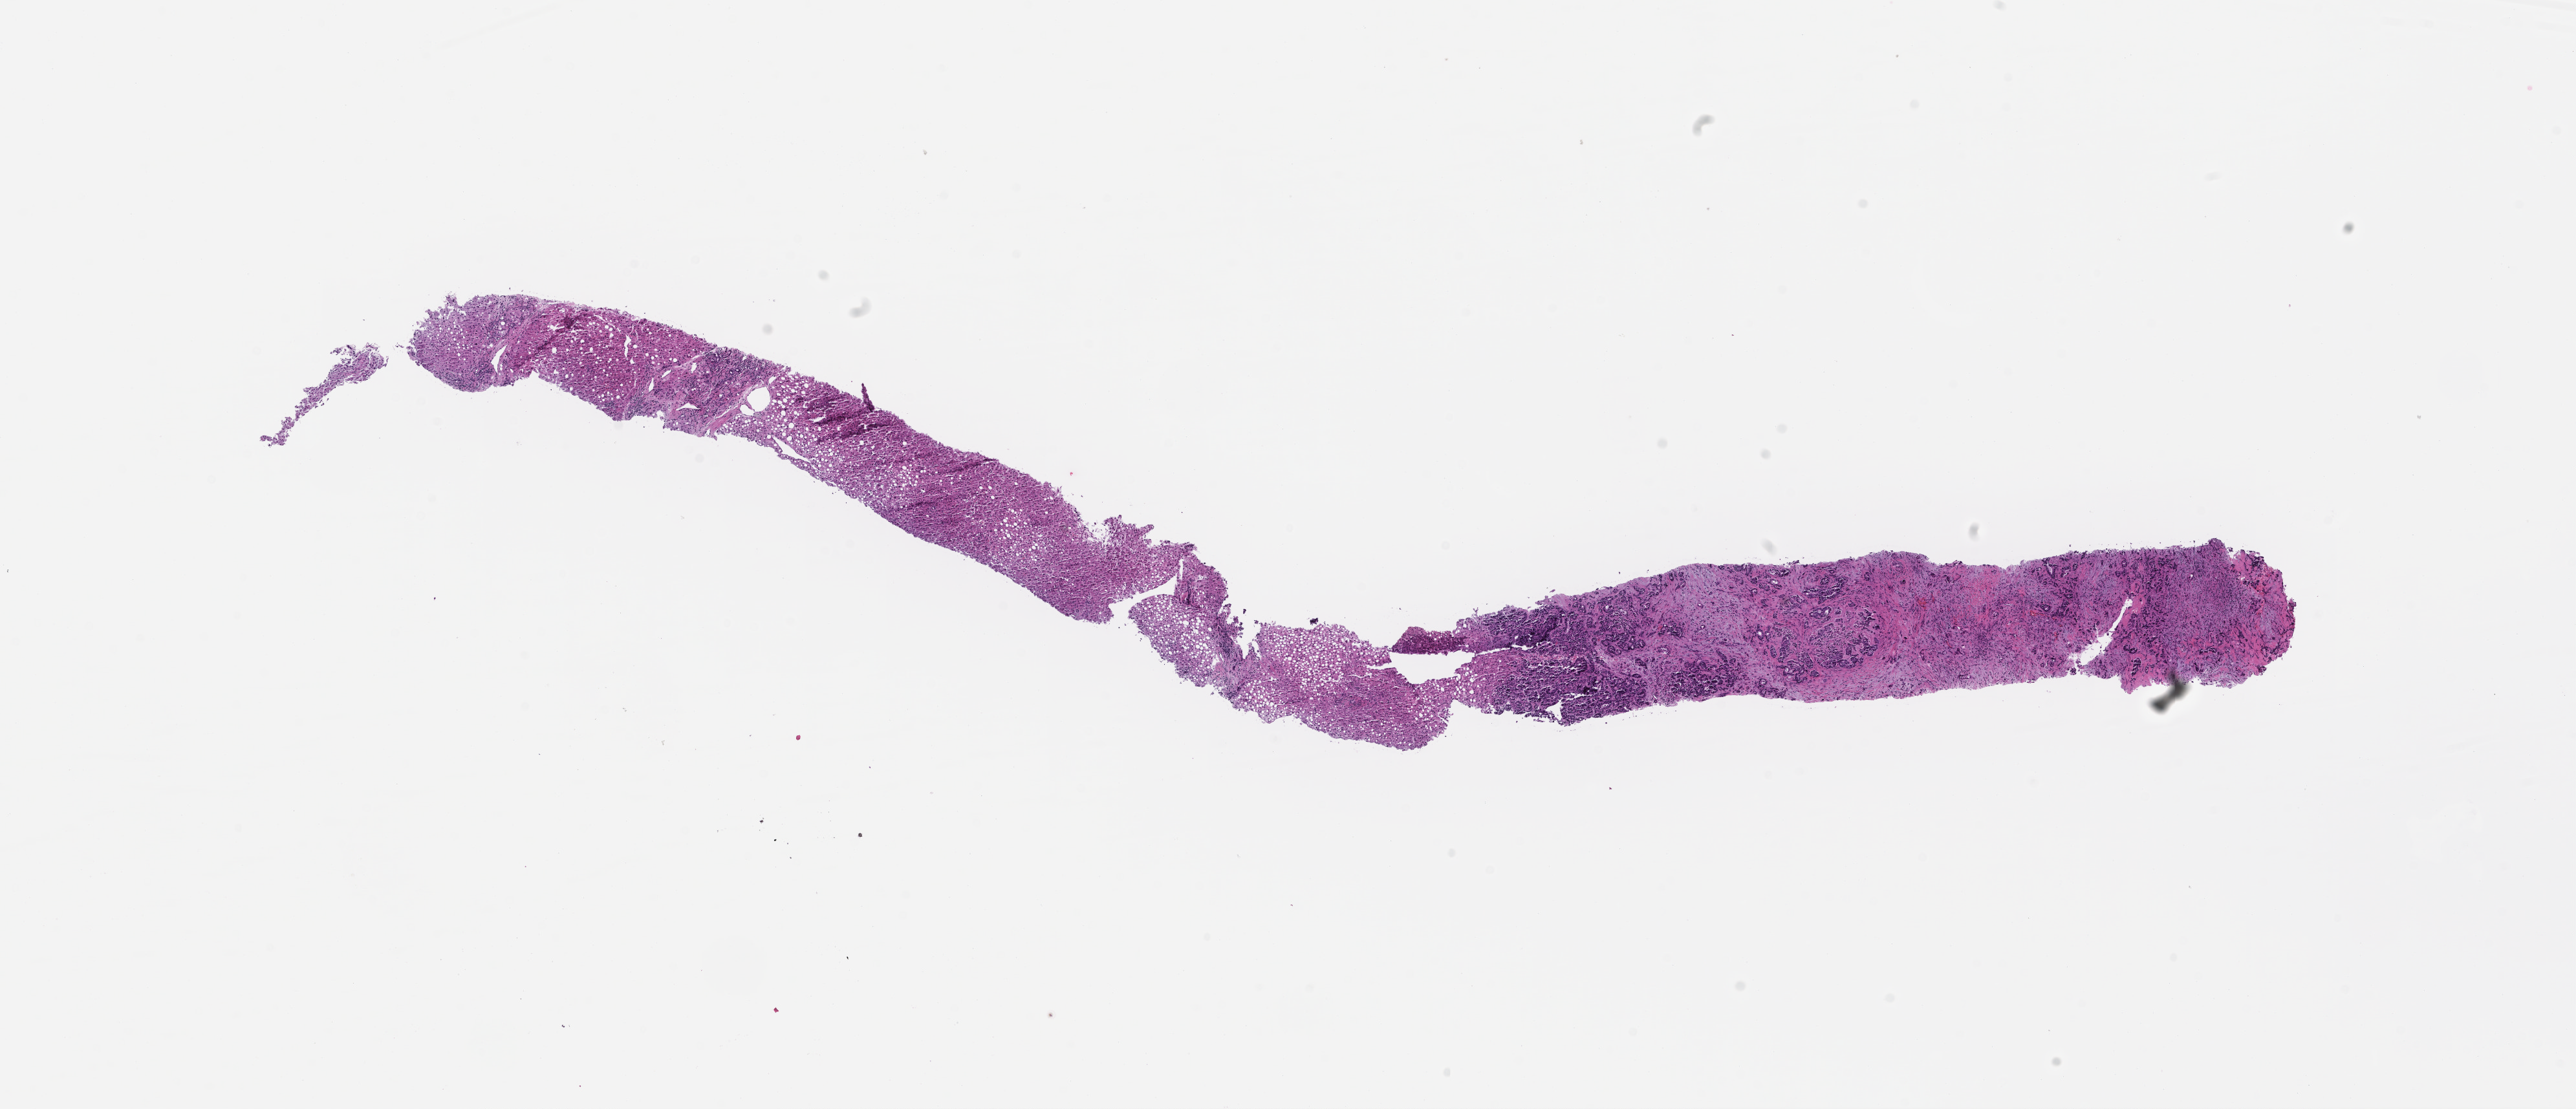
Whole-slide image, hematoxylin and eosin (H&E) stain — low-resolution overview of the scanned area, about 16.1 x 6.9 mm, formalin-fixed paraffin-embedded section, tissue site: colon, collected at baseline (before treatment). Female patient.
This section: primary tumor. Diagnosis: Colorectal Carcinoma.